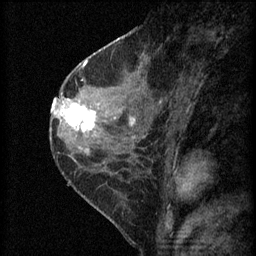
Breast MRI (dynamic contrast-enhanced), one sagittal slice. Position 29 of 60 along the scan axis. 3 images stored at this slice position (order not interpretable as contrast timing). 1.5 T. TE 4.2 ms, TR 8.2 ms. 2 mm slice thickness. 256 × 256 image matrix, field of view 180 × 180 mm. Female patient, age 45 years.
Outlined on this slice (semi-automatically segmented with operator editing):
- analysis volume of interest (the breast-tissue region the enhancement analysis was run in; not a lesion): bounding box <62,98,104,139> (left, top, right, bottom; pixels)
- tumour enhancement mask (voxels above the 70 % enhancement threshold inside the analysis volume of interest): <62,102,98,133>